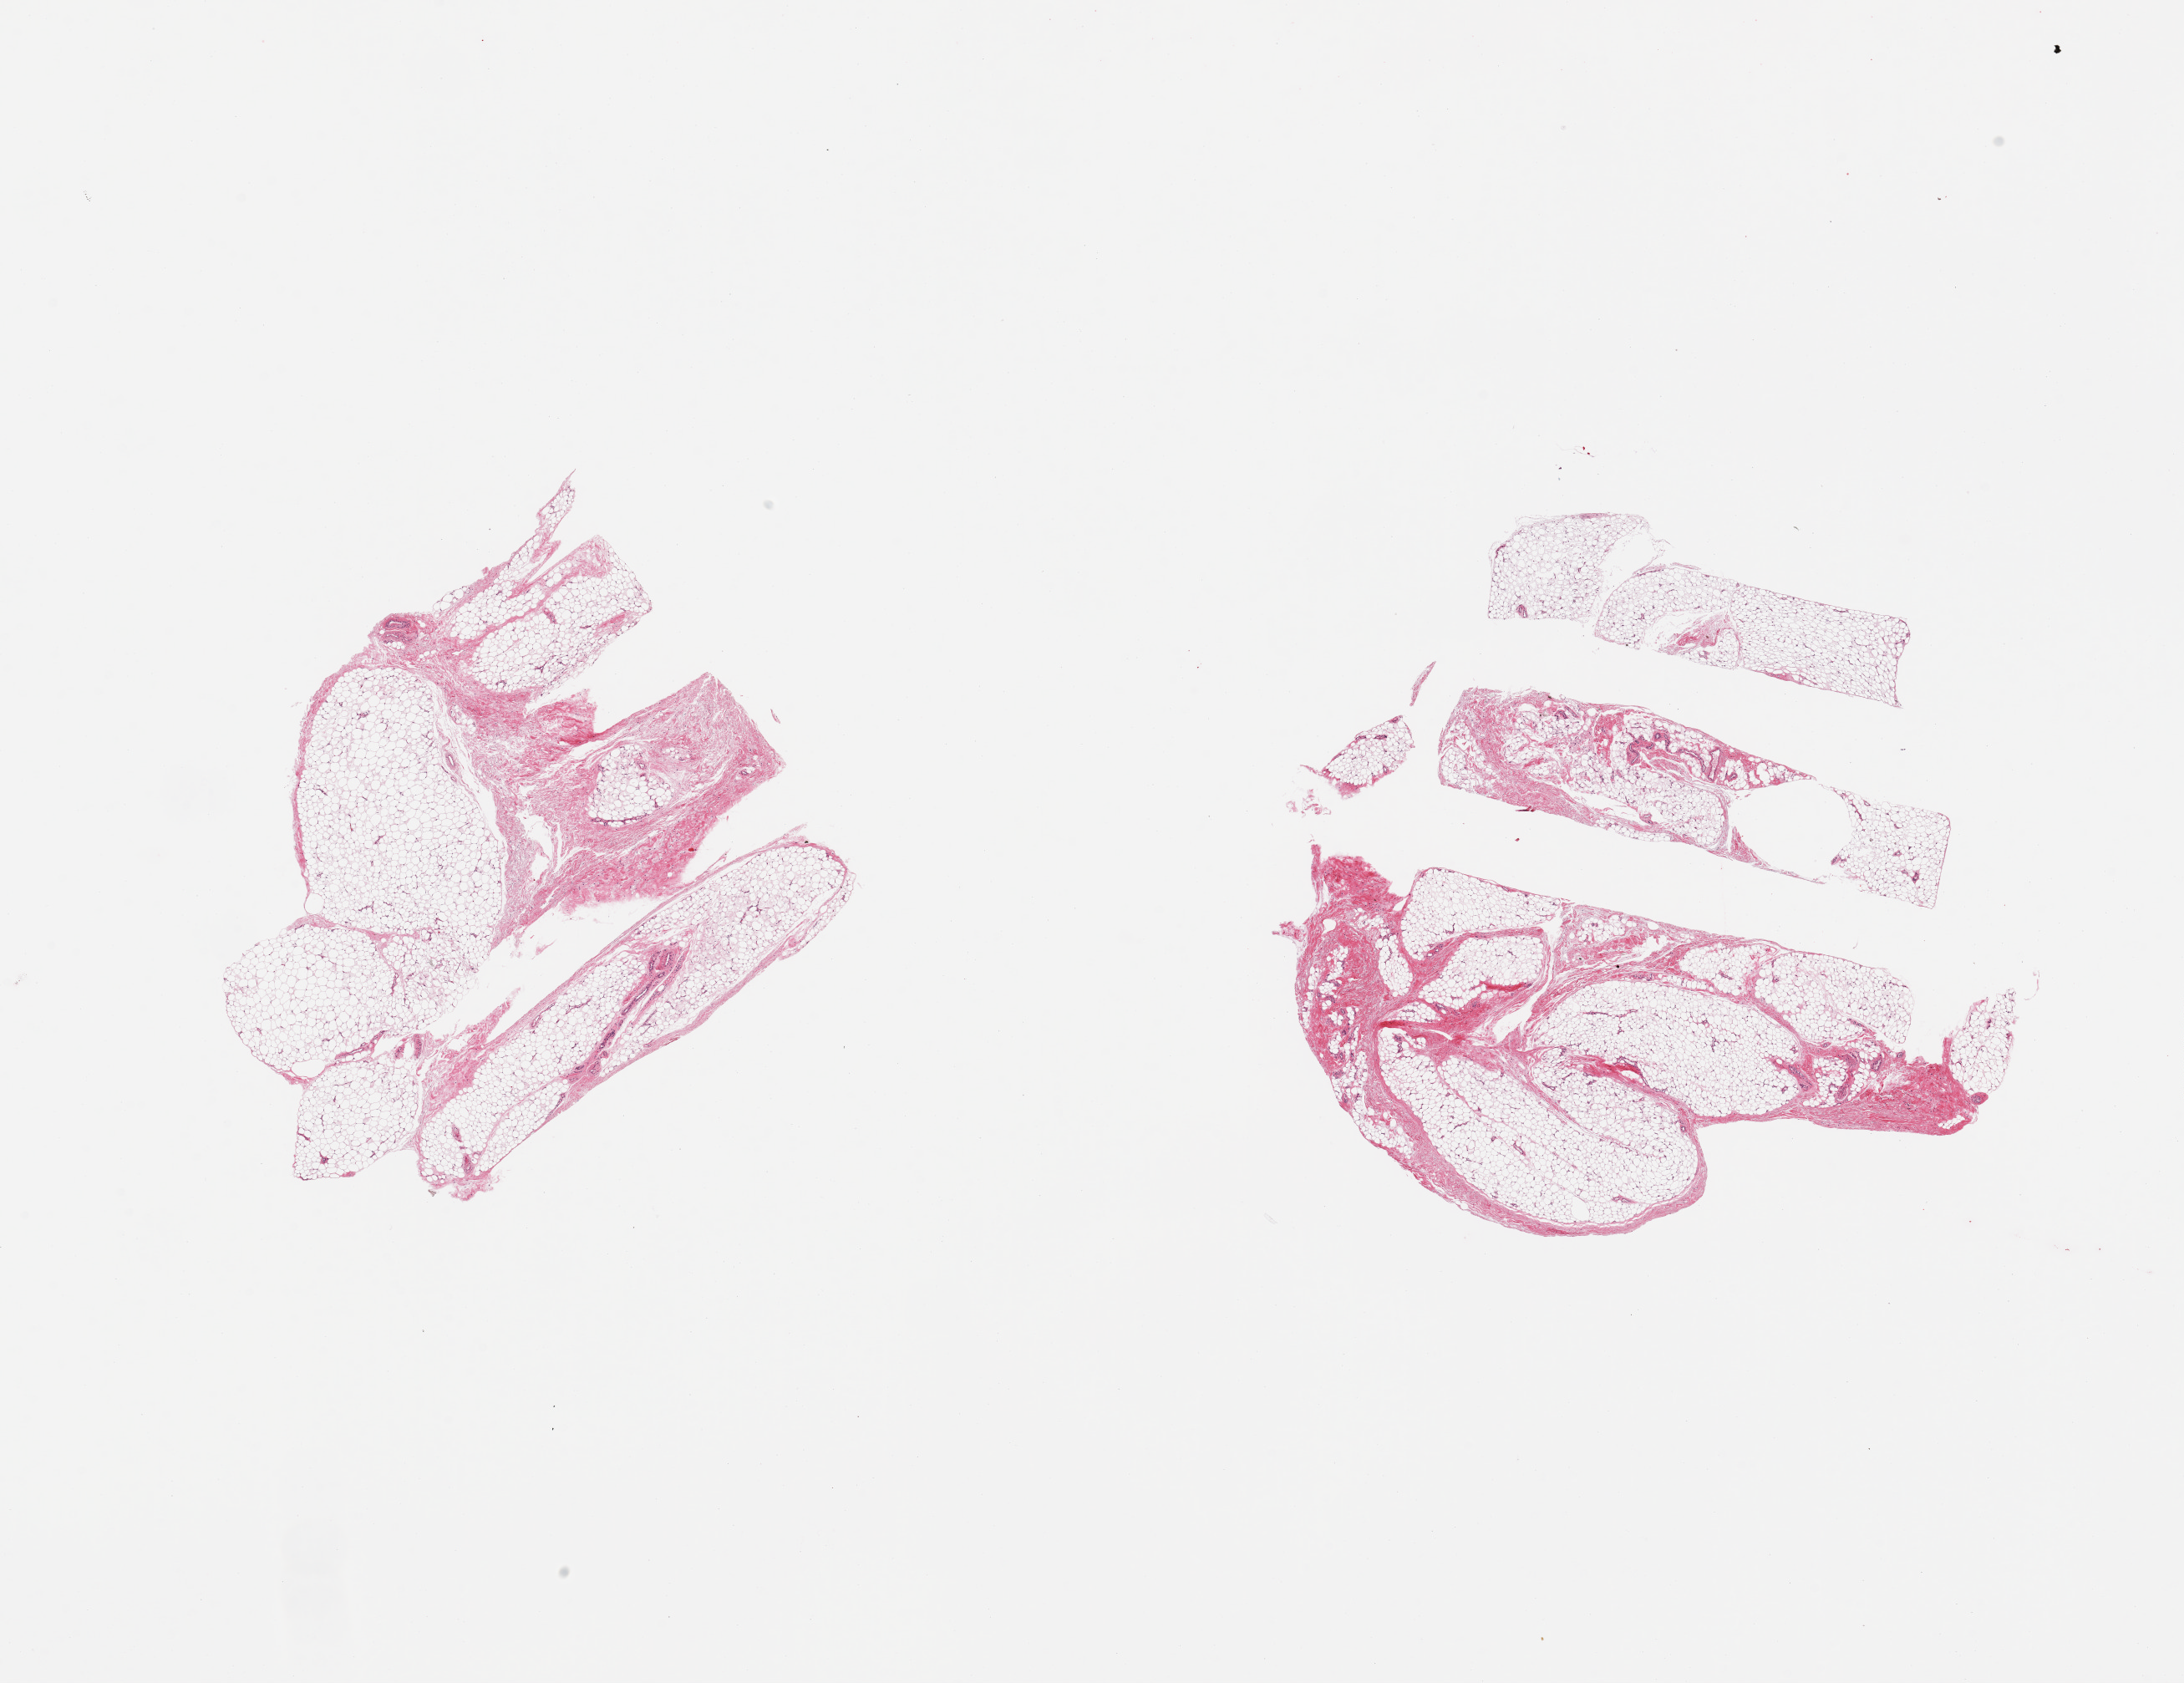
Digitized hematoxylin and eosin (H&E)-stained section — whole scanned area (about 20.7 x 15.9 mm) shown as a low-resolution overview; PAXgene-fixed paraffin-embedded (PFPE) section; target tissue: adipose tissue; tissue donor sample. Male donor.
• reviewer comment on this tissue sample: 2 pieces; 20% fibrous component